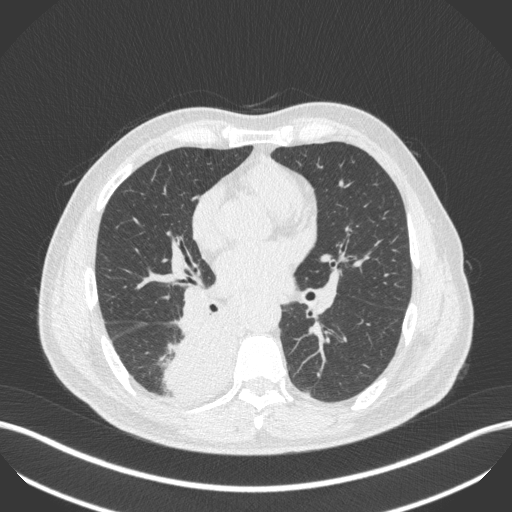
Chest CT, one axial slice; position 239 of 451 along the scan axis; lung window (W 1500 / L -600 HU); 1 mm slice thickness; 512 × 512 image matrix, field of view 400 × 400 mm. Male patient, age 61 years. From the clinical record (not read from this slice): clinical TNM (as recorded): T1 N0 M0; histopathological grade: G3.
Outlined on this slice (rectangle marked by the reading radiologist):
- lung tumour (recorded histology: small cell carcinoma): bounding box [x1, y1, x2, y2] px = [150, 306, 232, 397]